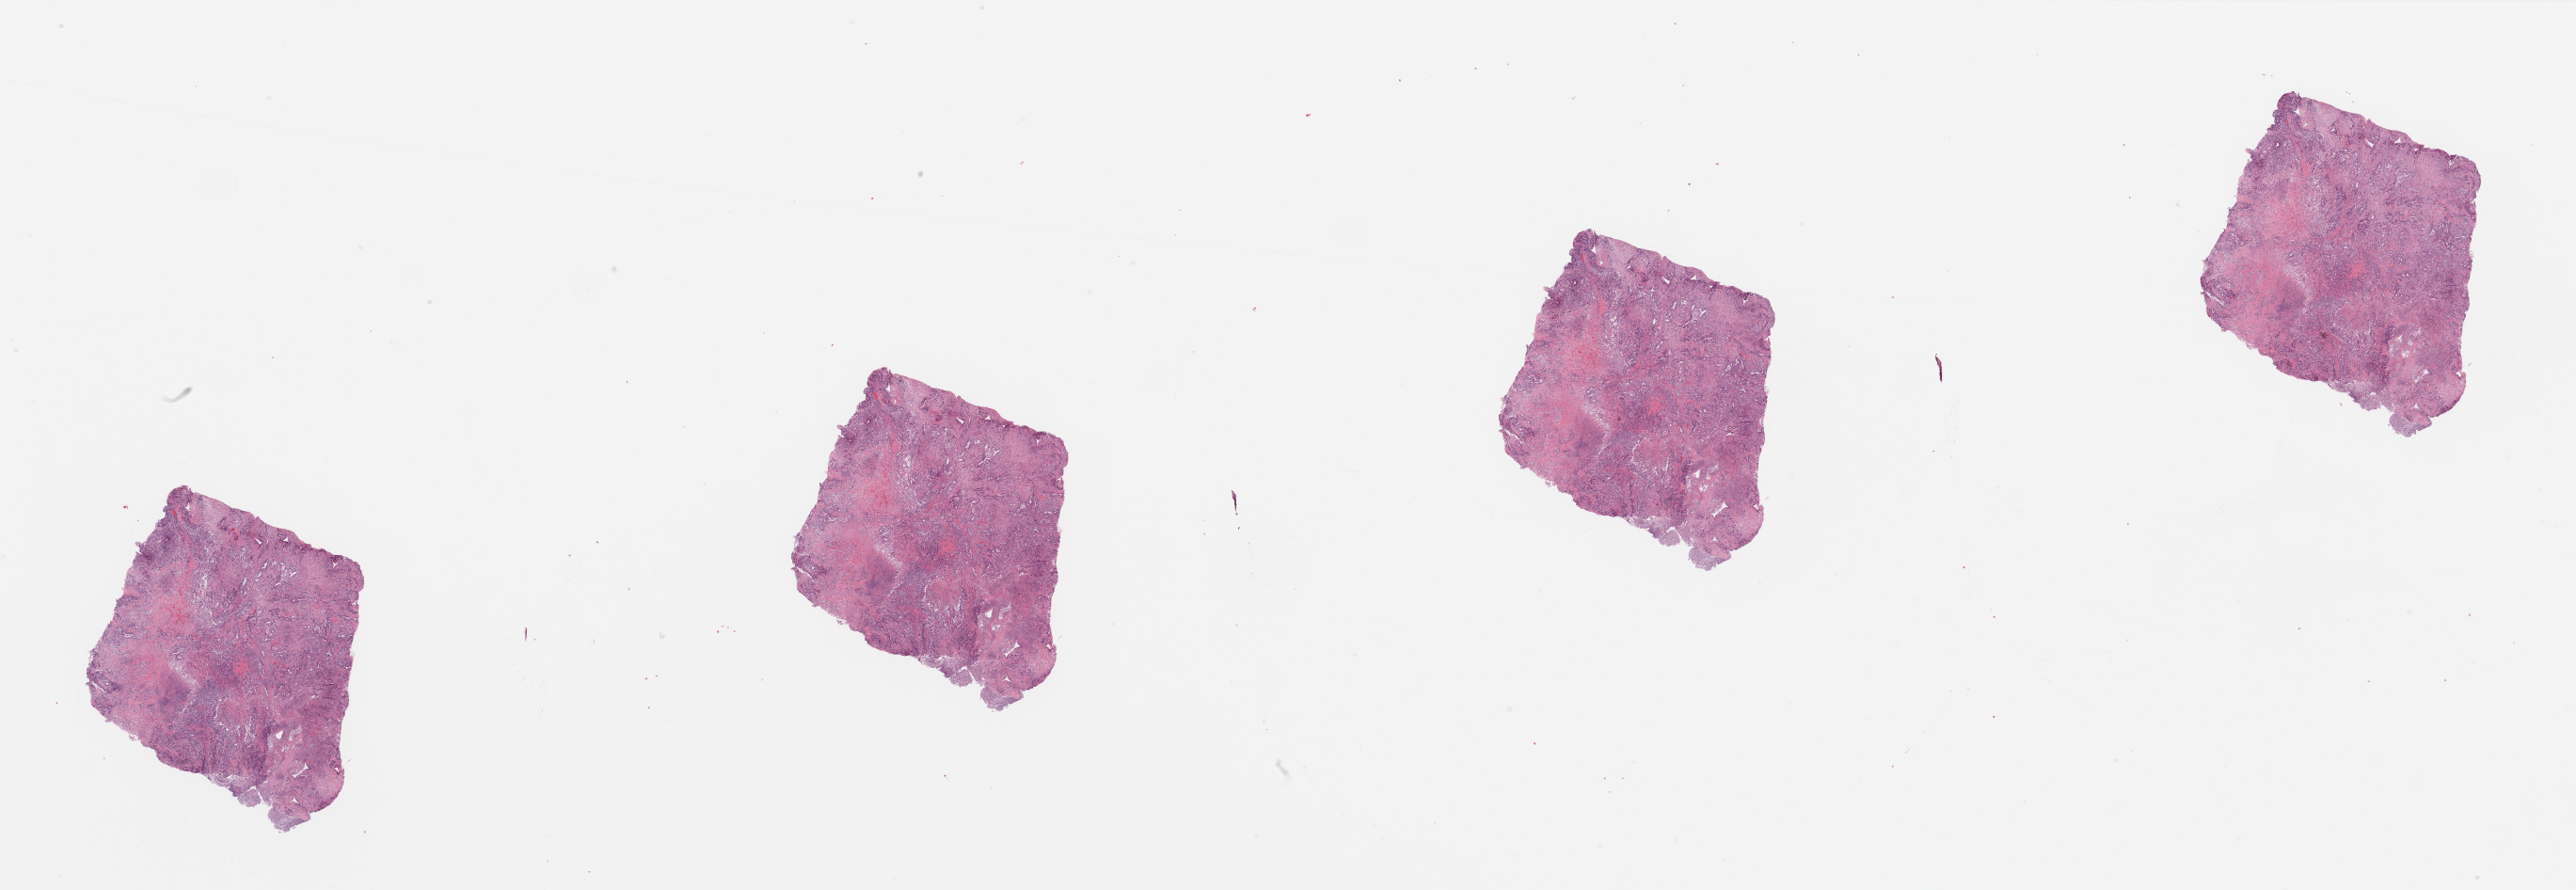
Digitized H&E tissue section (whole slide), shown as a low-resolution overview of the whole scanned area (about 43.3 x 15.0 mm), pancreas, tumour tissue. Female, 60 y/o. Histologic grade: G2 (moderately differentiated).
Diagnosis: Infiltrating duct carcinoma, NOS. AJCC pathologic stage: IIB. Primary tumour site (as recorded): head.